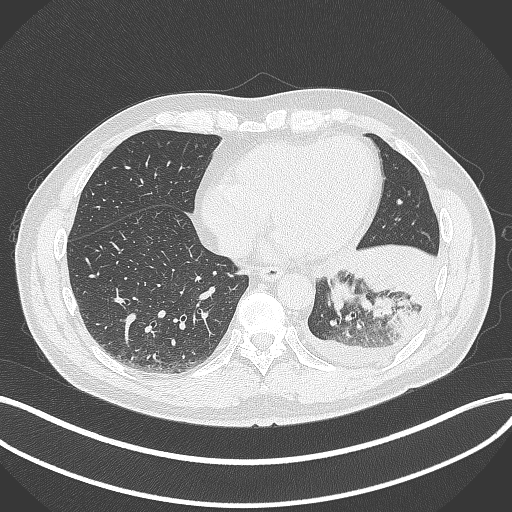
Chest CT, one axial slice. Slice 110 of 342 in the series (ordered by position). Lung window (W 1500 / L -600 HU). 1 mm slice thickness. 512 × 512 image matrix, field of view 400 × 400 mm. Male patient, age 58 years. Case-level facts recorded for this patient, not image findings: clinical TNM (as recorded): T3 N1 M1b; histopathological grade: G3.
Outlined on this slice (bounding box drawn by a radiologist):
- lung tumour (recorded histology: small cell carcinoma): box from (x=323, y=274) to (x=362, y=325) px